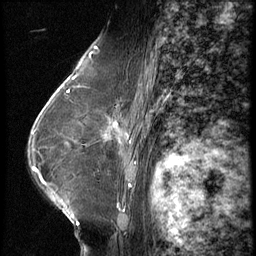
Breast MRI (dynamic contrast-enhanced), one sagittal slice. Position 40 of 62 along the scan axis. 3 images stored at this slice position (order not interpretable as contrast timing). 1.5 T. TE 4.2 ms, TR 9 ms. 2.5 mm slice thickness. 256 × 256 image matrix, field of view 180 × 180 mm. Patient: female, 65 years. Case-level facts recorded for this patient, not image findings: setting: breast cancer imaged before/during neoadjuvant chemotherapy; receptor status: HR-positive, HER2-negative.
Annotated regions visible in this slice (semi-automatic segmentation, software-assisted and operator-edited):
- analysis volume of interest (the breast-tissue region the enhancement analysis was run in; not a lesion): bounding box (x1, y1, x2, y2) in pixels: (104, 104, 154, 161)
- tumour enhancement mask (voxels above the 140 % enhancement threshold inside the analysis volume of interest): (104, 135, 131, 142)